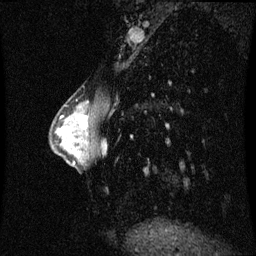
Breast MRI (dynamic contrast-enhanced), one sagittal slice; position 24 of 60 along the scan axis; dynamic contrast-enhanced series, image 2 of 3 at this slice position (ordered by acquisition); 1.5 T; TE 4.2 ms, TR 8.9 ms; 256 × 256 image matrix, field of view 210 × 210 mm. Patient: female, 33 years. From the clinical record (not read from this slice): setting: breast cancer imaged before/during neoadjuvant chemotherapy; receptor status: HER2-positive.
Structures marked on this image (semi-automatically segmented with operator editing):
- analysis volume of interest (the breast-tissue region the enhancement analysis was run in; not a lesion): bounding box [x1, y1, x2, y2] px = [66, 103, 94, 141]
- tumour enhancement mask (voxels above the 70 % enhancement threshold inside the analysis volume of interest): [79, 117, 88, 130]